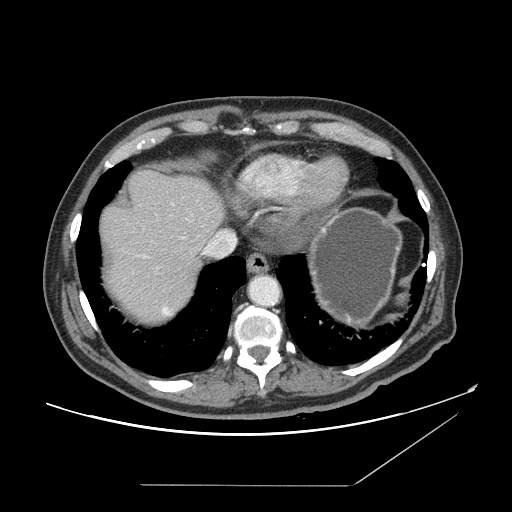
Contrast-enhanced abdominal CT, one axial slice; slice 135 of 166 in the series (ordered by position); intravenous contrast given; soft-tissue window (W 400 / L 40 HU); 2.5 mm slice thickness; 512 × 512 image matrix, field of view 416 × 416 mm. Male patient, age 80 years. From the clinical record (not read from this slice): diagnosis: colorectal cancer liver metastases, imaged before liver resection; multiple liver metastases: no; largest metastasis: 2.2 cm; disease in both lobes: no.
Outlined on this slice (manually delineated by an expert):
- hepatic veins: bounding box (x1, y1, x2, y2) in pixels: (144, 231, 236, 257)
- liver: (99, 170, 224, 324)
- planned liver remnant (the part of the liver to remain after resection): (99, 170, 225, 259)